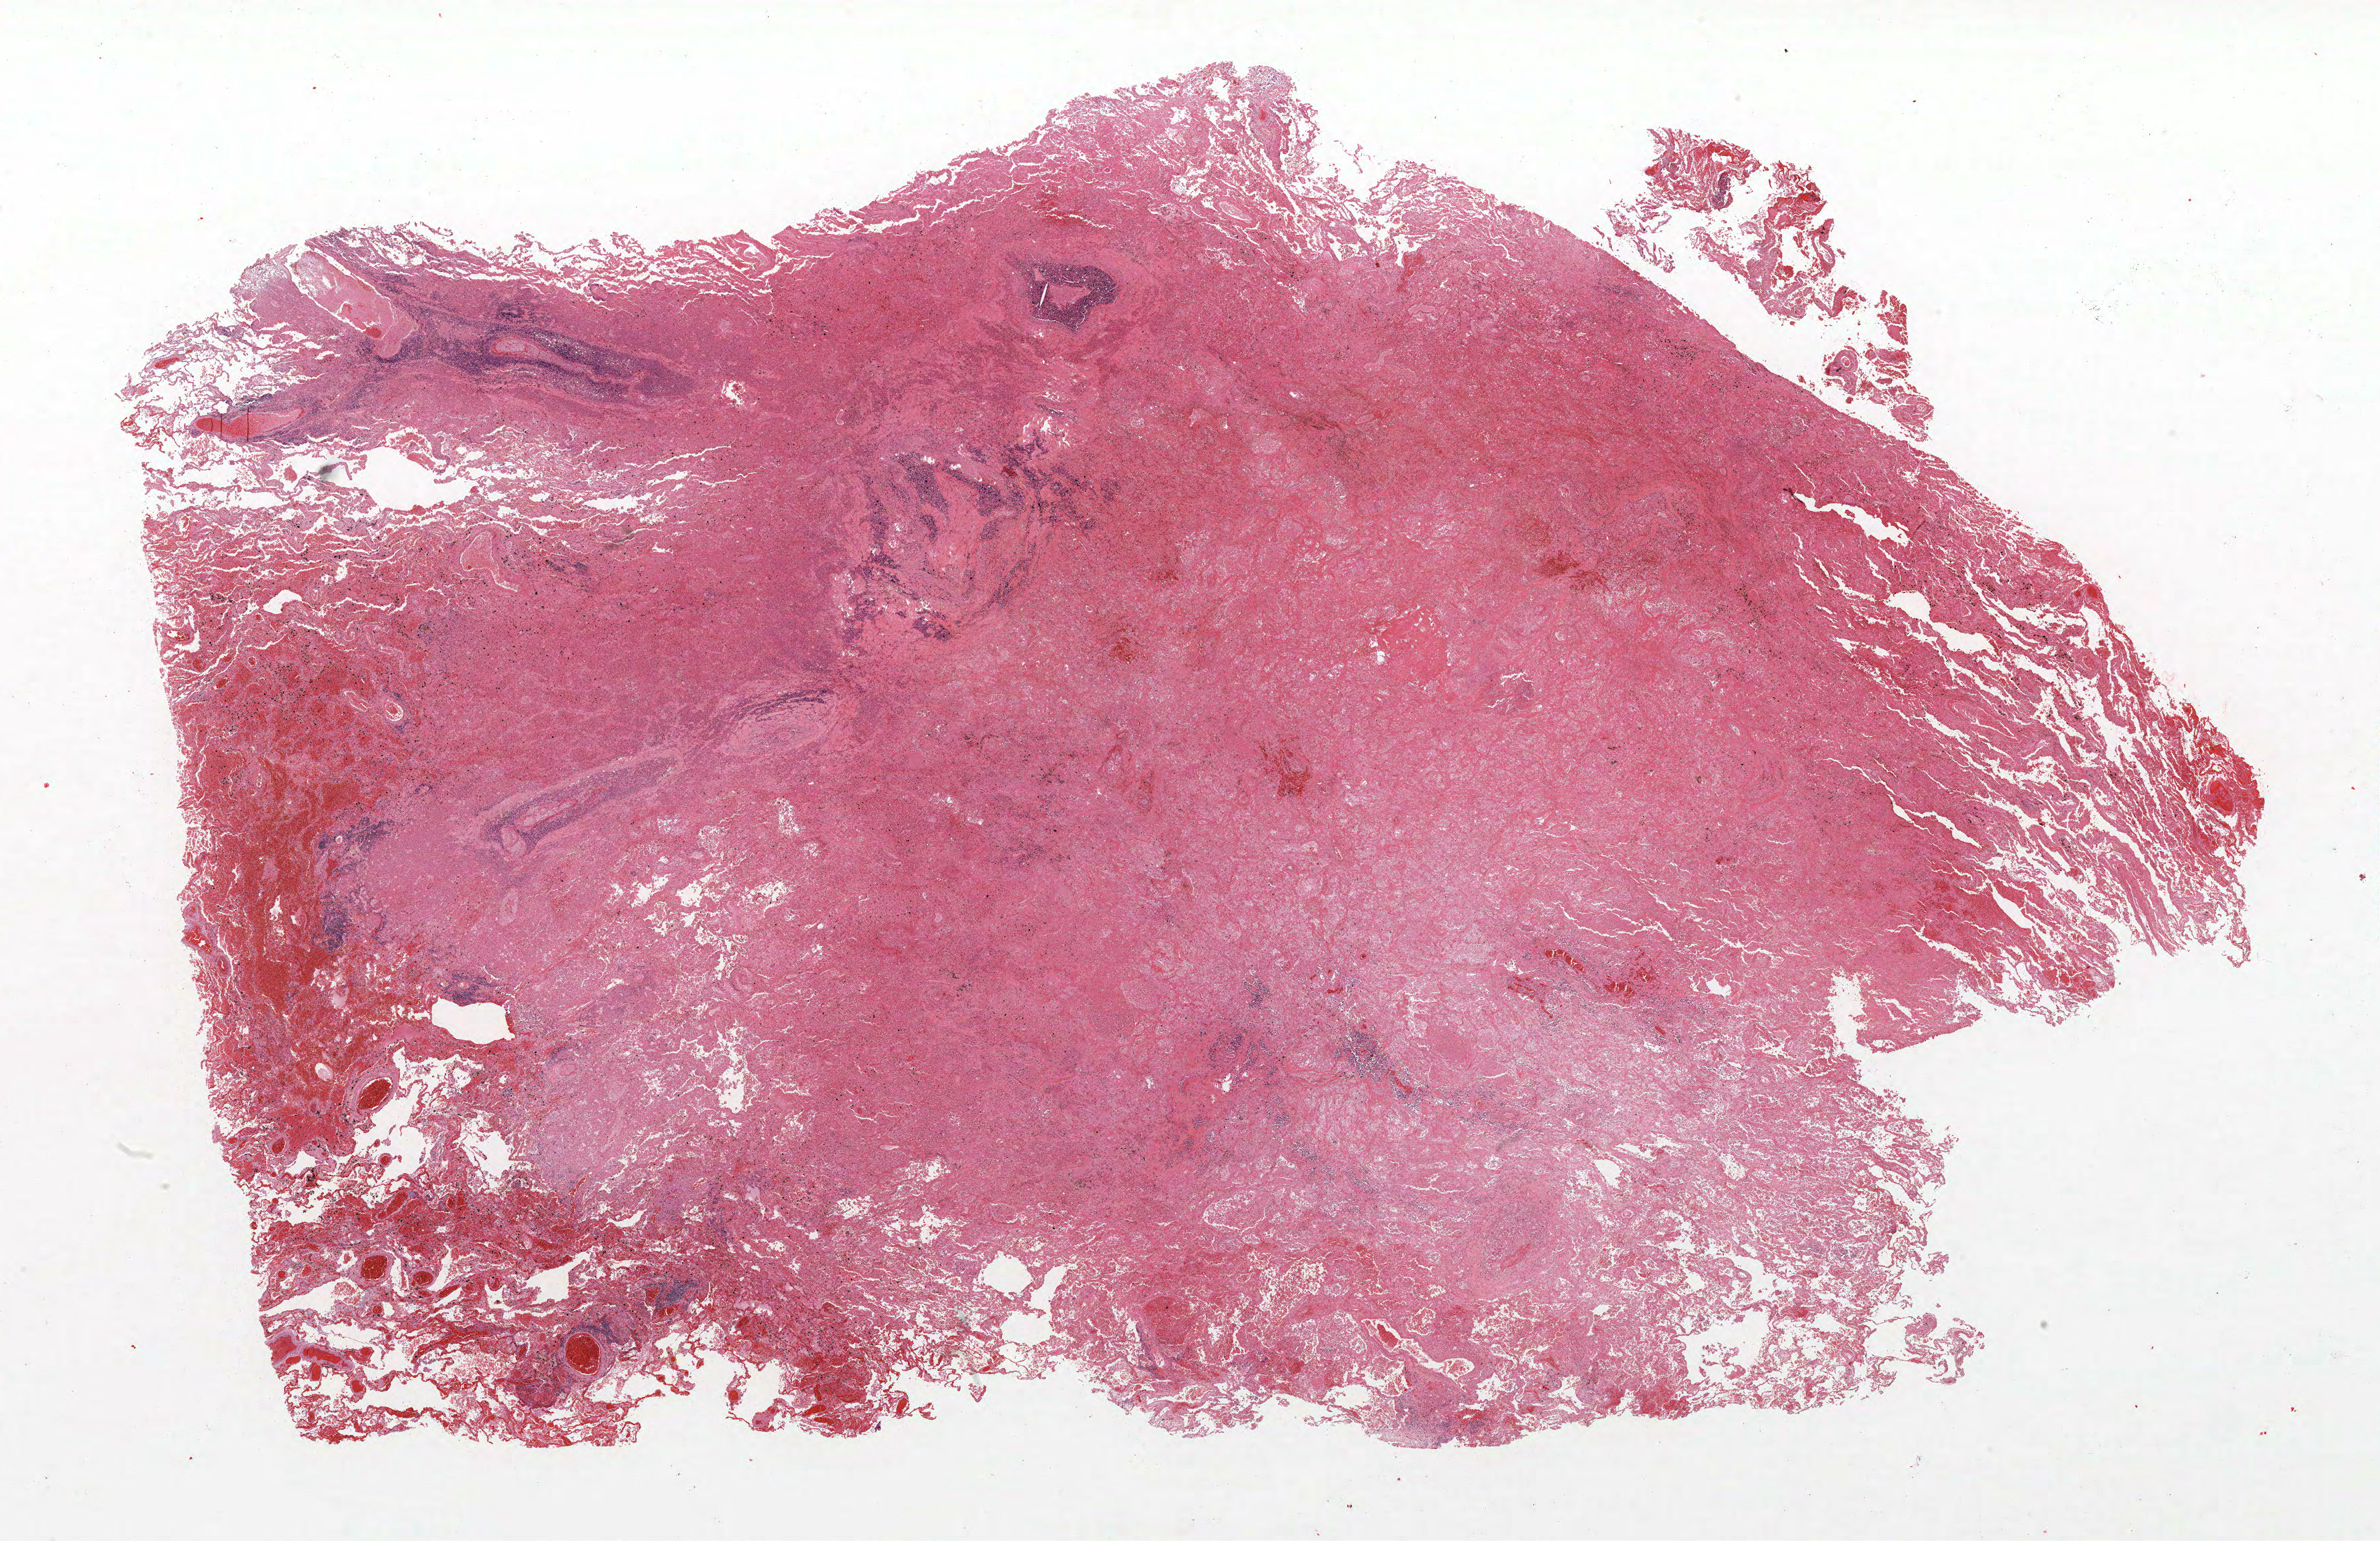
Whole-slide histology image, H&E — shown as a low-resolution overview of the whole scanned area (about 28.6 x 18.5 mm), FFPE section, lung. Male, age 67 at enrolment. Current smoker at enrolment.
Primary tumour location (clinical record): right middle lobe. ICD-O-3 topography: middle lobe of lung (C34.2). Participant's lung-cancer diagnosis: Small cell carcinoma, NOS (ICD-O-3 8041/3). Stage (AJCC 6th edition): IA. Tumour size (pathology): 20 mm.